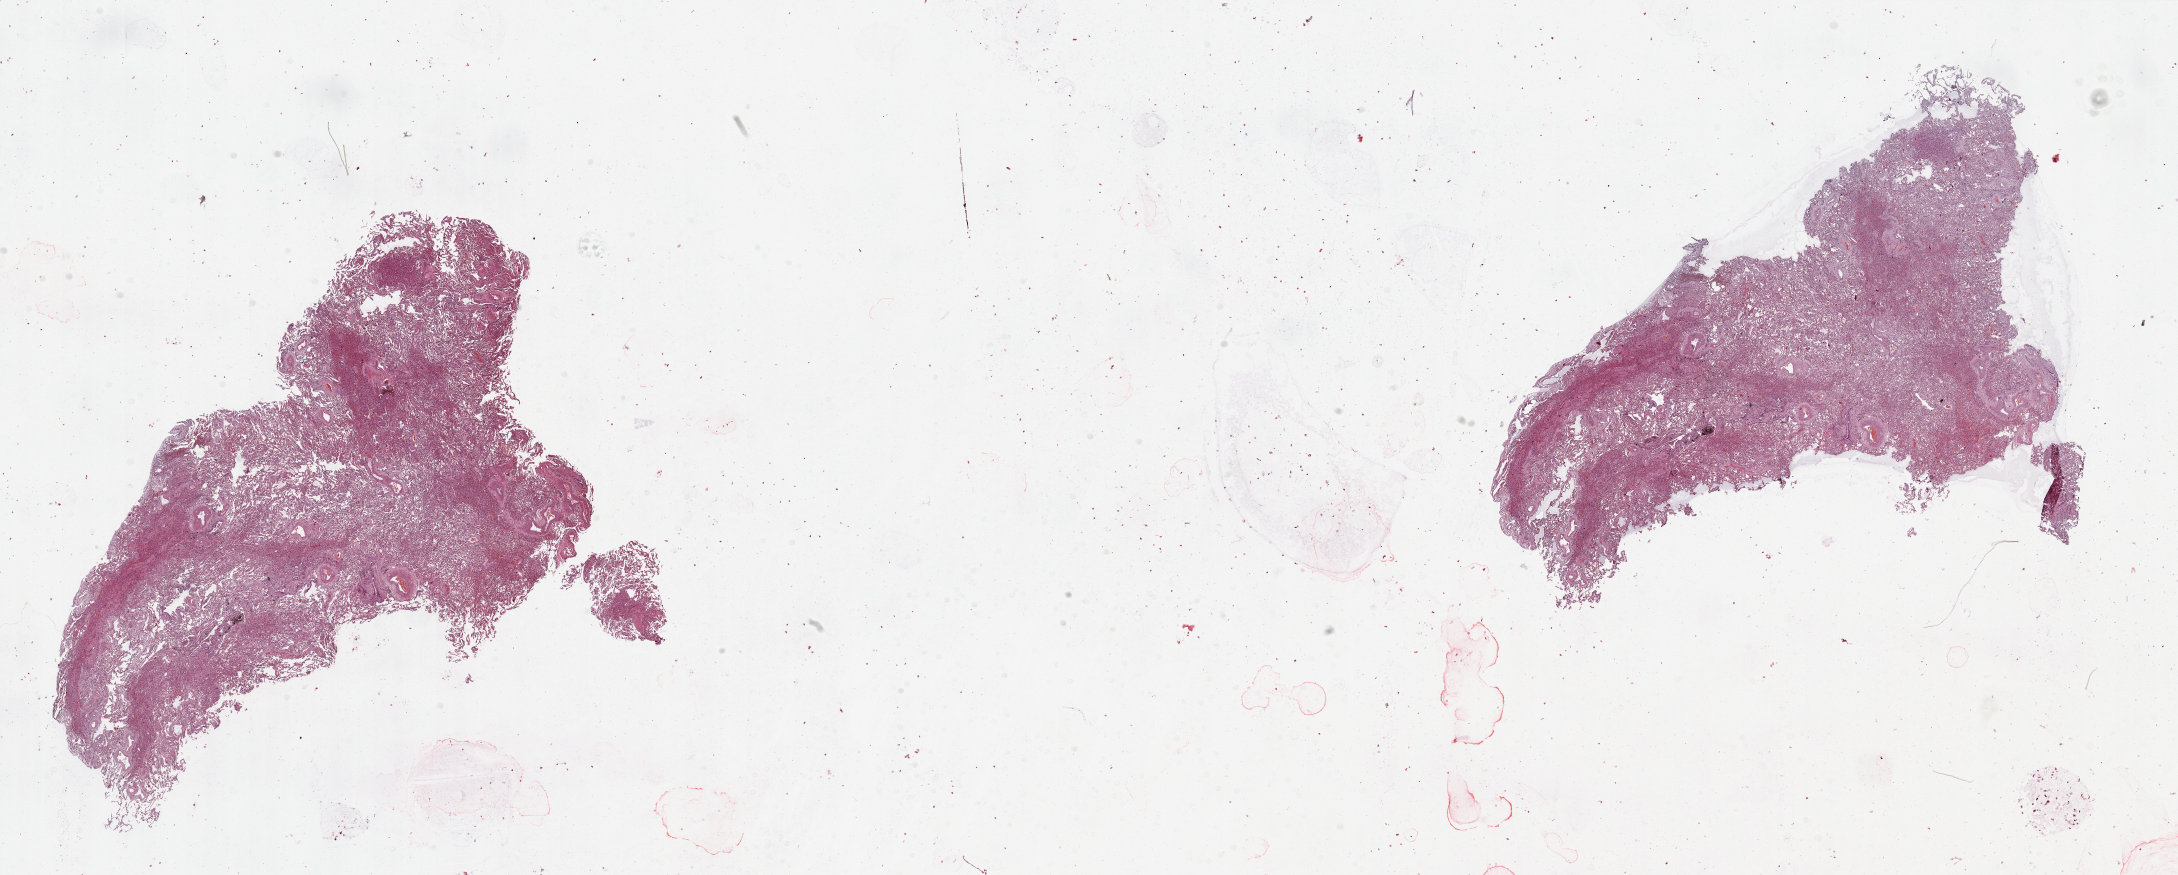
Digitized Hematoxylin and eosin (H&E) stained tissue section (whole slide) — whole scanned area (about 34.5 x 13.8 mm, from a 20x scan) shown as a low-resolution overview; normal (non-tumour) tissue sample, sampled site: lung. Patient: male, age 56 years.
This section: normal (non-tumour) tissue from the same patient. Patient diagnosis: Adenocarcinoma, NOS.